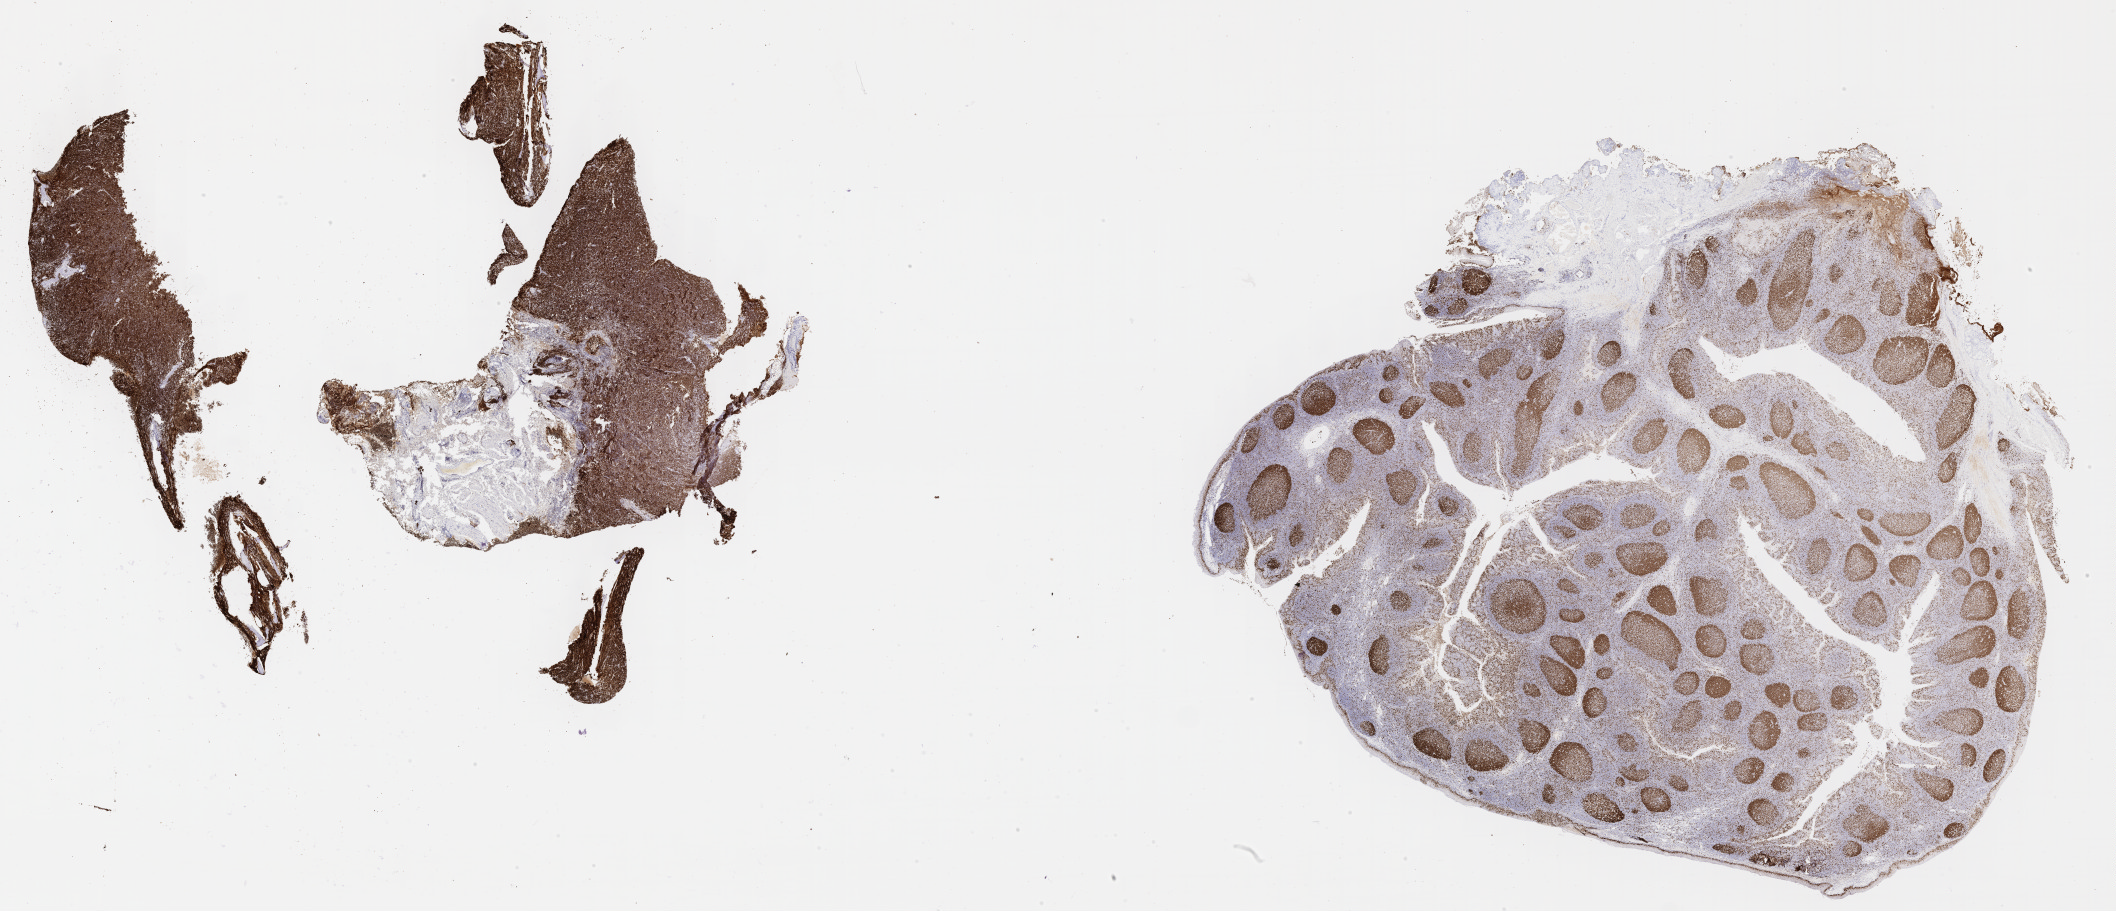
Immunohistochemistry (IHC) whole-slide image stained for Ki-67 — a low-resolution overview of the entire scanned area, about 34.2 x 14.7 mm. Tumor tissue. Site: cranium. Male patient; age at initial diagnosis 8 years.
Histologic diagnosis: Burkitt lymphoma, NOS.